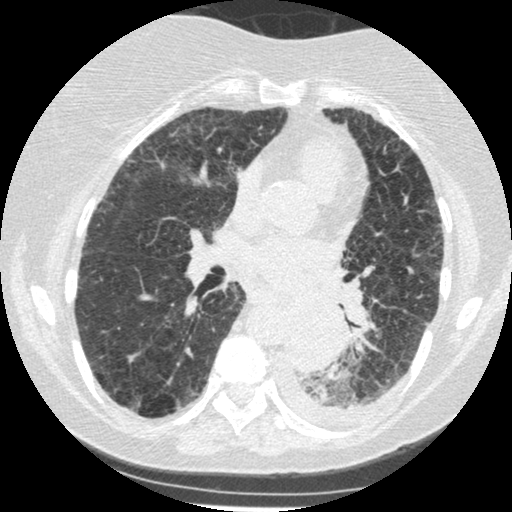
Axial slice from a low-dose chest CT screening exam, third screening round (two years after baseline), lung window (W 1500 / L -600 HU), 1.25 mm slice thickness, standard (soft-tissue) reconstruction kernel (STANDARD), slice 218 of 341 in the series, 512 × 512 image matrix, field of view 310 × 310 mm. Female, age 60 years at enrolment. Former smoker at enrolment.
Expert reader's lesion annotation, bounding box [x1, y1, x2, y2] px = [273, 305, 342, 375]. Screening reader's record for this exam (one nodule recorded; not confirmed to be the boxed lesion): non-calcified nodule or mass ≥4 mm, left lower lobe, 54 × 38 mm, smooth margins, soft tissue attenuation, pre-existing on the prior screen: yes; interval growth: yes. Lung cancer was diagnosed 15 days after this screen: small cell carcinoma, NOS, left lower lobe, undifferentiated (G4), stage IV (AJCC 6th edition), 69 mm at pathology.